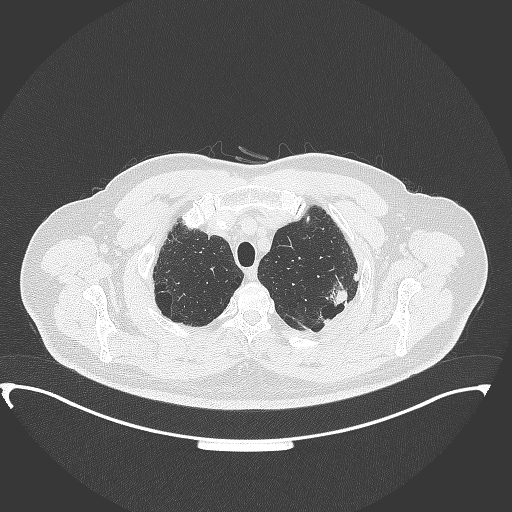
Chest CT, one axial slice; position 314 of 350 along the scan axis; reconstruction kernel B70f; lung window (W 1500 / L -600 HU); 1 mm slice thickness; 512 × 512 image matrix. Patient: male, 64 years. From the clinical record (not read from this slice): clinical TNM (as recorded): T1c N1 M1.
Outlined on this slice (bounding box drawn by a radiologist):
- lung tumour (recorded histology: adenocarcinoma): bounding box [x1, y1, x2, y2] px = [331, 273, 351, 311]